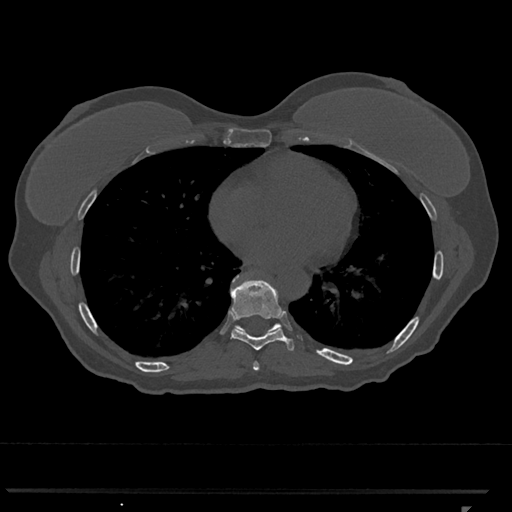
CT including the spine, one axial slice. Position 657 of 793 along the scan axis. Reconstruction kernel Br40s/3. 120 kVp. Bone window (W 1800 / L 400 HU). 0.5 mm slice thickness. 512 × 512 image matrix, field of view 380 × 380 mm. Female patient, age 62 years. From the clinical record (not read from this slice): primary cancer: renal.
Outlined on this slice (semi-automatically segmented with operator editing):
- T7 vertebra: bounding box <253,362,260,371> (left, top, right, bottom; pixels)
- T8 vertebra: <230,279,294,351>
- T9 vertebra: <233,275,282,332>